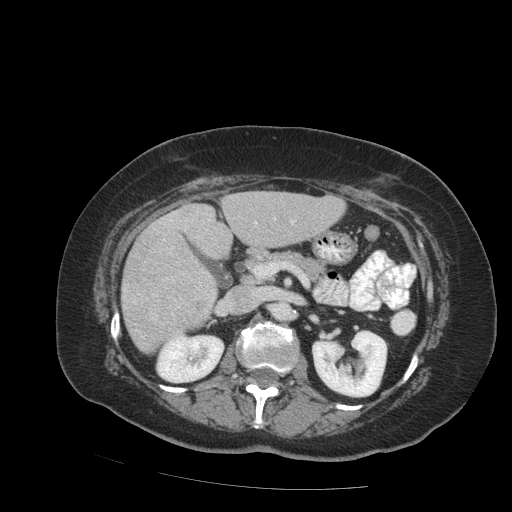
Contrast-enhanced abdominal CT (liver protocol), one axial slice; position 39 of 99 along the scan axis; reconstruction kernel STANDARD; 140 kVp; soft-tissue window (W 400 / L 40 HU); 2.5 mm slice thickness; 512 × 512 image matrix. From the clinical record (not read from this slice): diagnosis: hepatocellular carcinoma (patient treated with transarterial chemoembolisation; whether this scan precedes or follows treatment is not stated here); TNM stage (as recorded): Stage-IVB; Child-Pugh class: A; tumour differentiation: moderately differentiated; tumour nodularity: uninodular.
Outlined on this slice (semi-automatic segmentation, software-assisted and operator-edited):
- liver parenchyma outside the tumour (the mass and vessels are separate outlines, so this box may not span the whole liver): bounding box (x1, y1, x2, y2) in pixels: (121, 190, 344, 352)
- liver vessels: (170, 219, 294, 224)